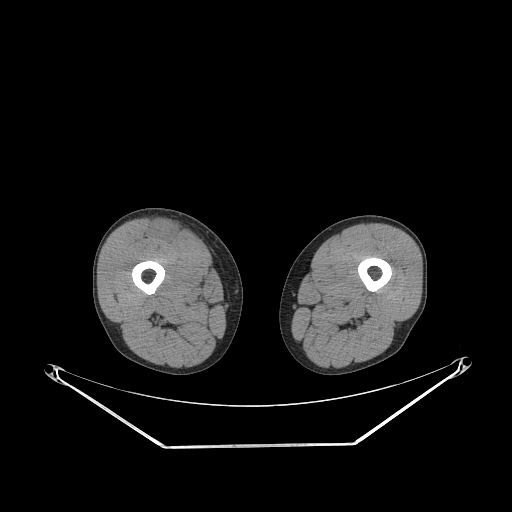
CT of an extremity soft-tissue mass (from a PET/CT study), one axial slice. Position 240 of 311 along the scan axis. Reconstruction kernel STANDARD. 140 kVp. Soft-tissue window (W 400 / L 40 HU). 3.75 mm slice thickness. 512 × 512 image matrix. Male patient. From the clinical record (not read from this slice): histological type: pleiomorphic leiomyosarcoma; grade: intermediate; site of the primary tumour: right thigh.
Annotated regions visible in this slice (expert contour drawn on MRI and transferred to this co-registered scan by the dataset authors):
- gross tumour volume including surrounding oedema: bounding box [x1, y1, x2, y2] px = [151, 221, 182, 243]